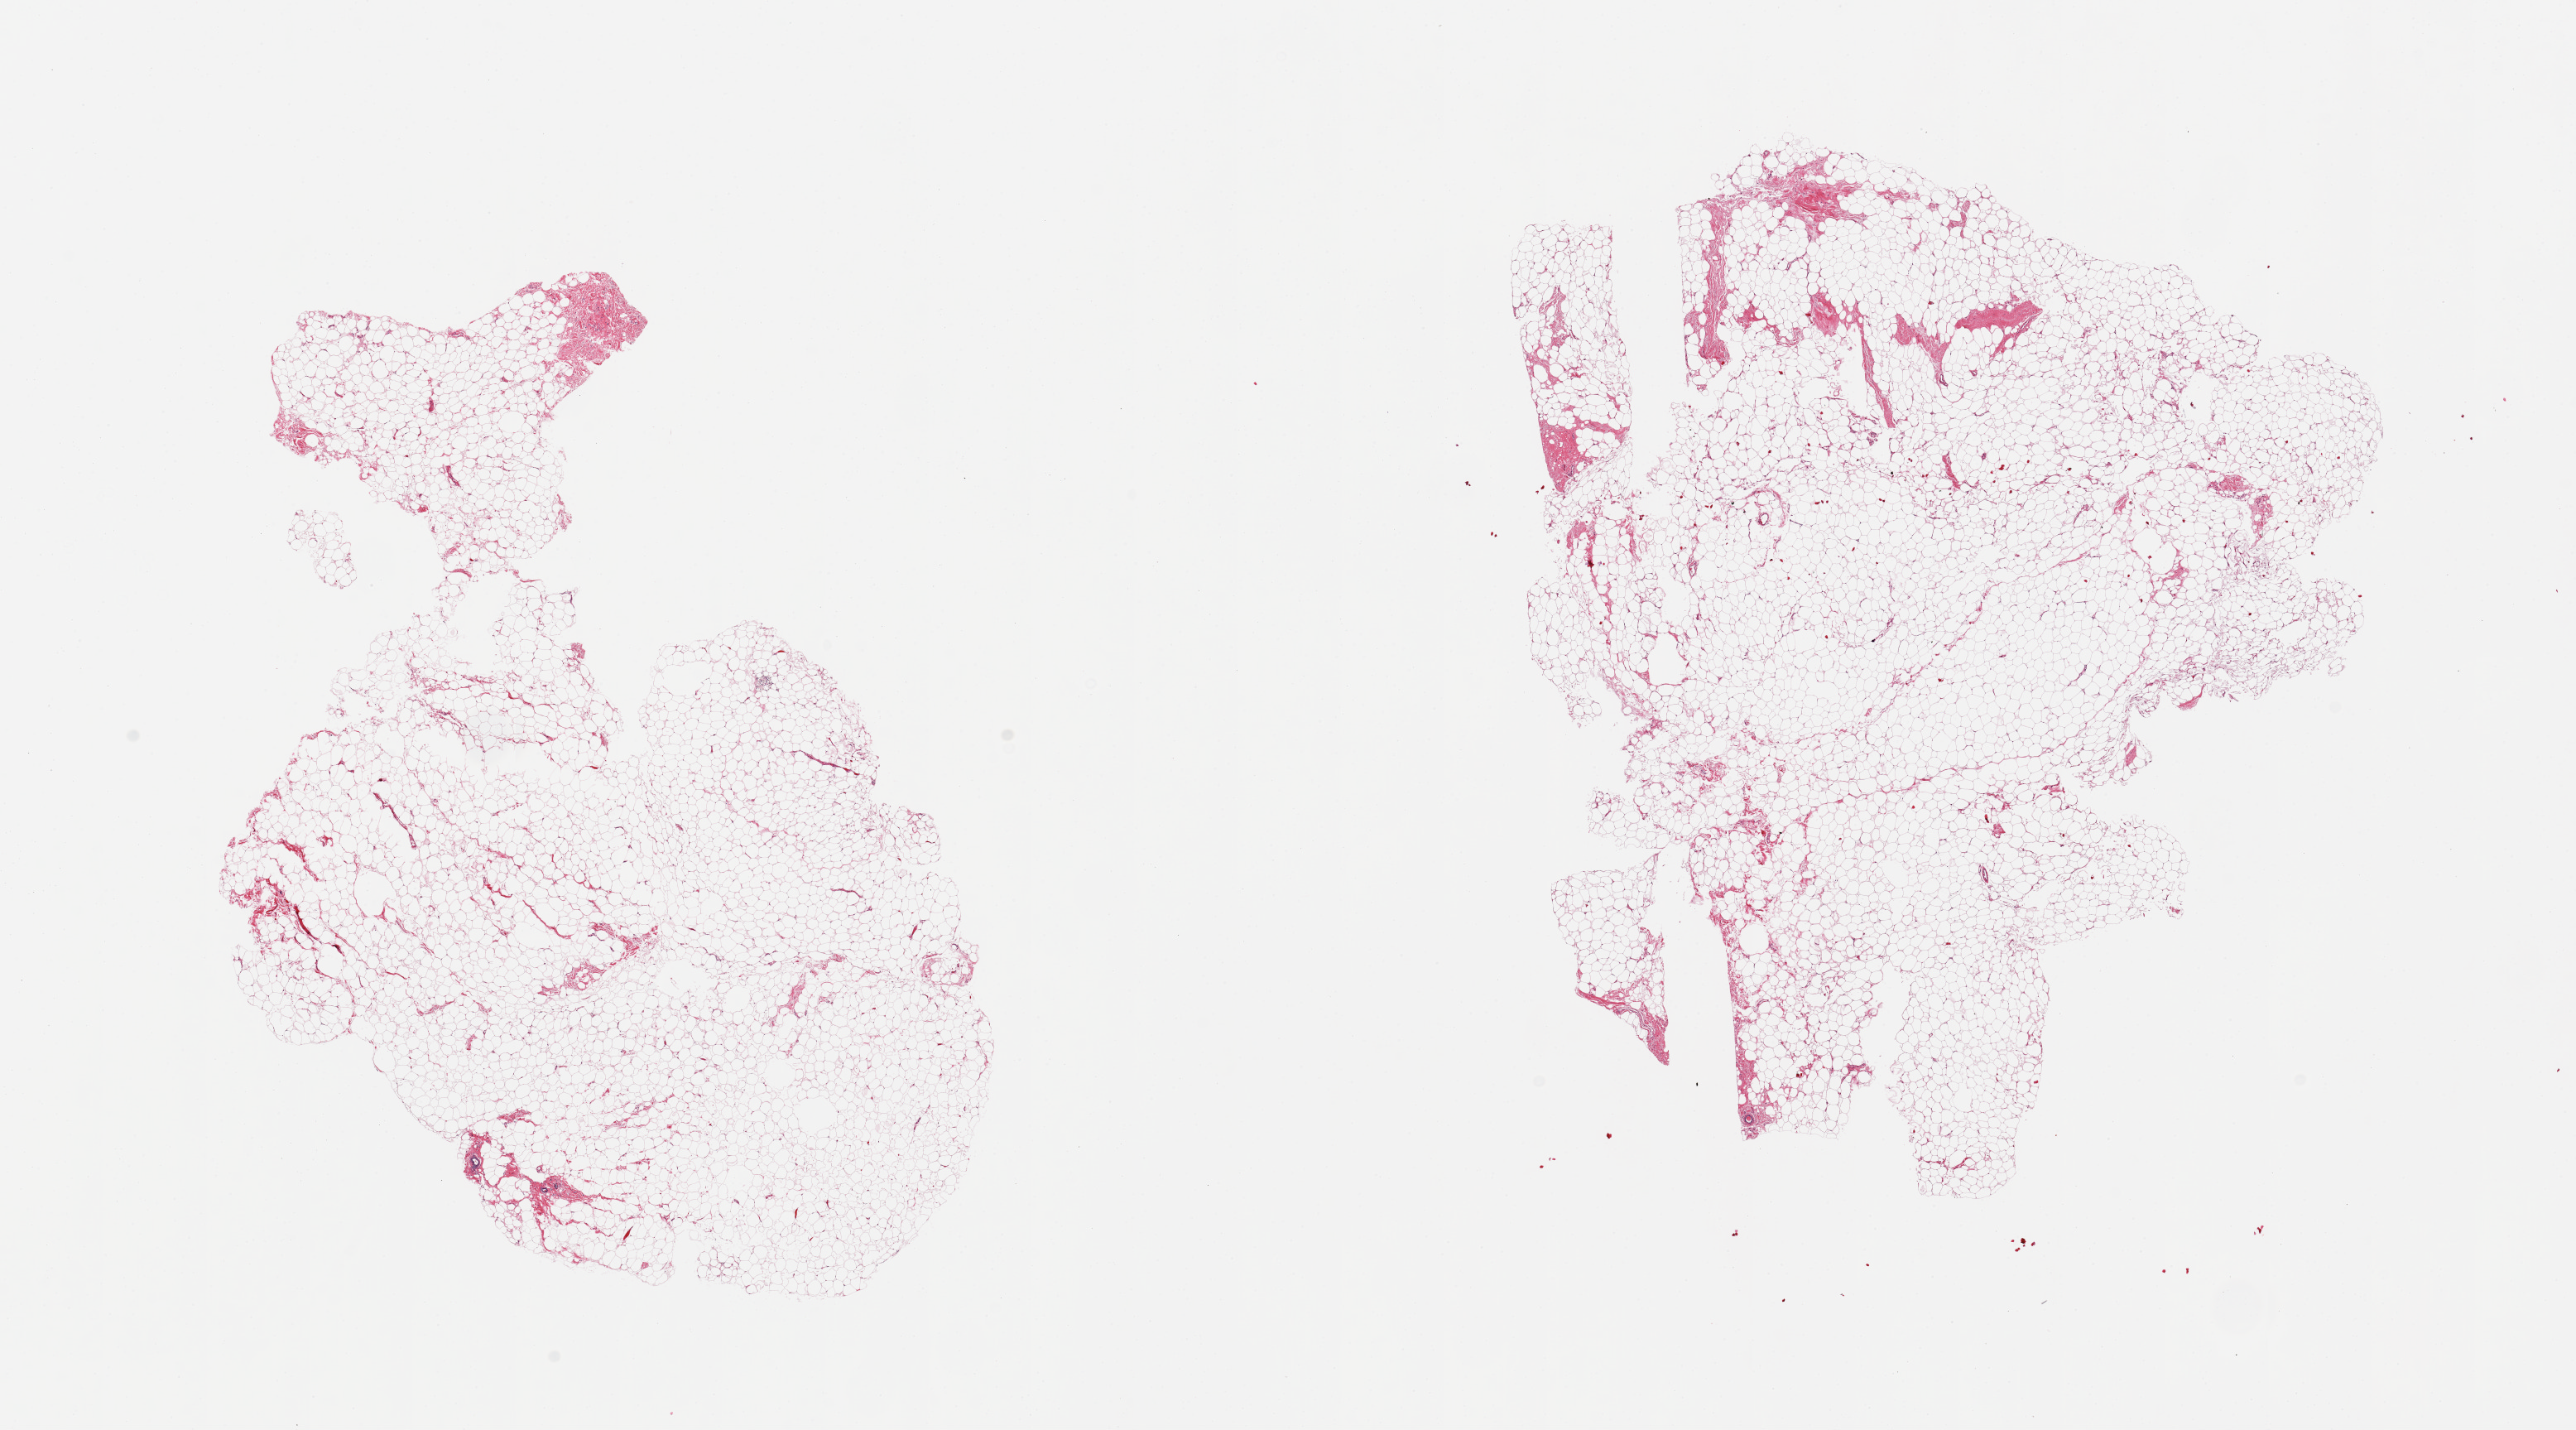
Digitized hematoxylin and eosin (H&E)-stained section, brightfield — shown as a low-resolution overview of the whole scanned area (about 24.6 x 13.7 mm), PAXgene-fixed, paraffin-embedded tissue, section of breast (target tissue), donor tissue sample. Donor: female.
- pathologist's review note for this sample: 2 pieces; adipose tissue with rare mammary duct